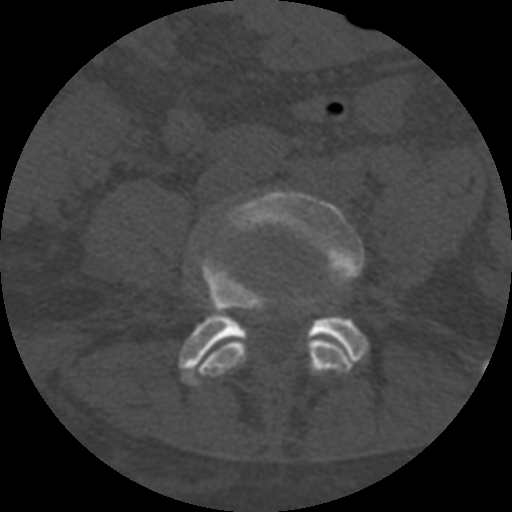
CT including the spine, one axial slice. Position 196 of 708 along the scan axis. 120 kVp. One of 3 acquisitions stored at this slice position. Bone window (W 1800 / L 400 HU). 1.25 mm slice thickness. 512 × 512 image matrix, field of view 160 × 160 mm. Patient age 55 years. Case-level facts recorded for this patient, not image findings: primary cancer: colon; vertebrae with lytic lesions (as recorded): T12, L1, L5.
Structures marked on this image (semi-automatically segmented with operator editing):
- L4 vertebra: box from (x=200, y=190) to (x=364, y=377) px
- L5 vertebra: (x=179, y=259)–(x=369, y=386)